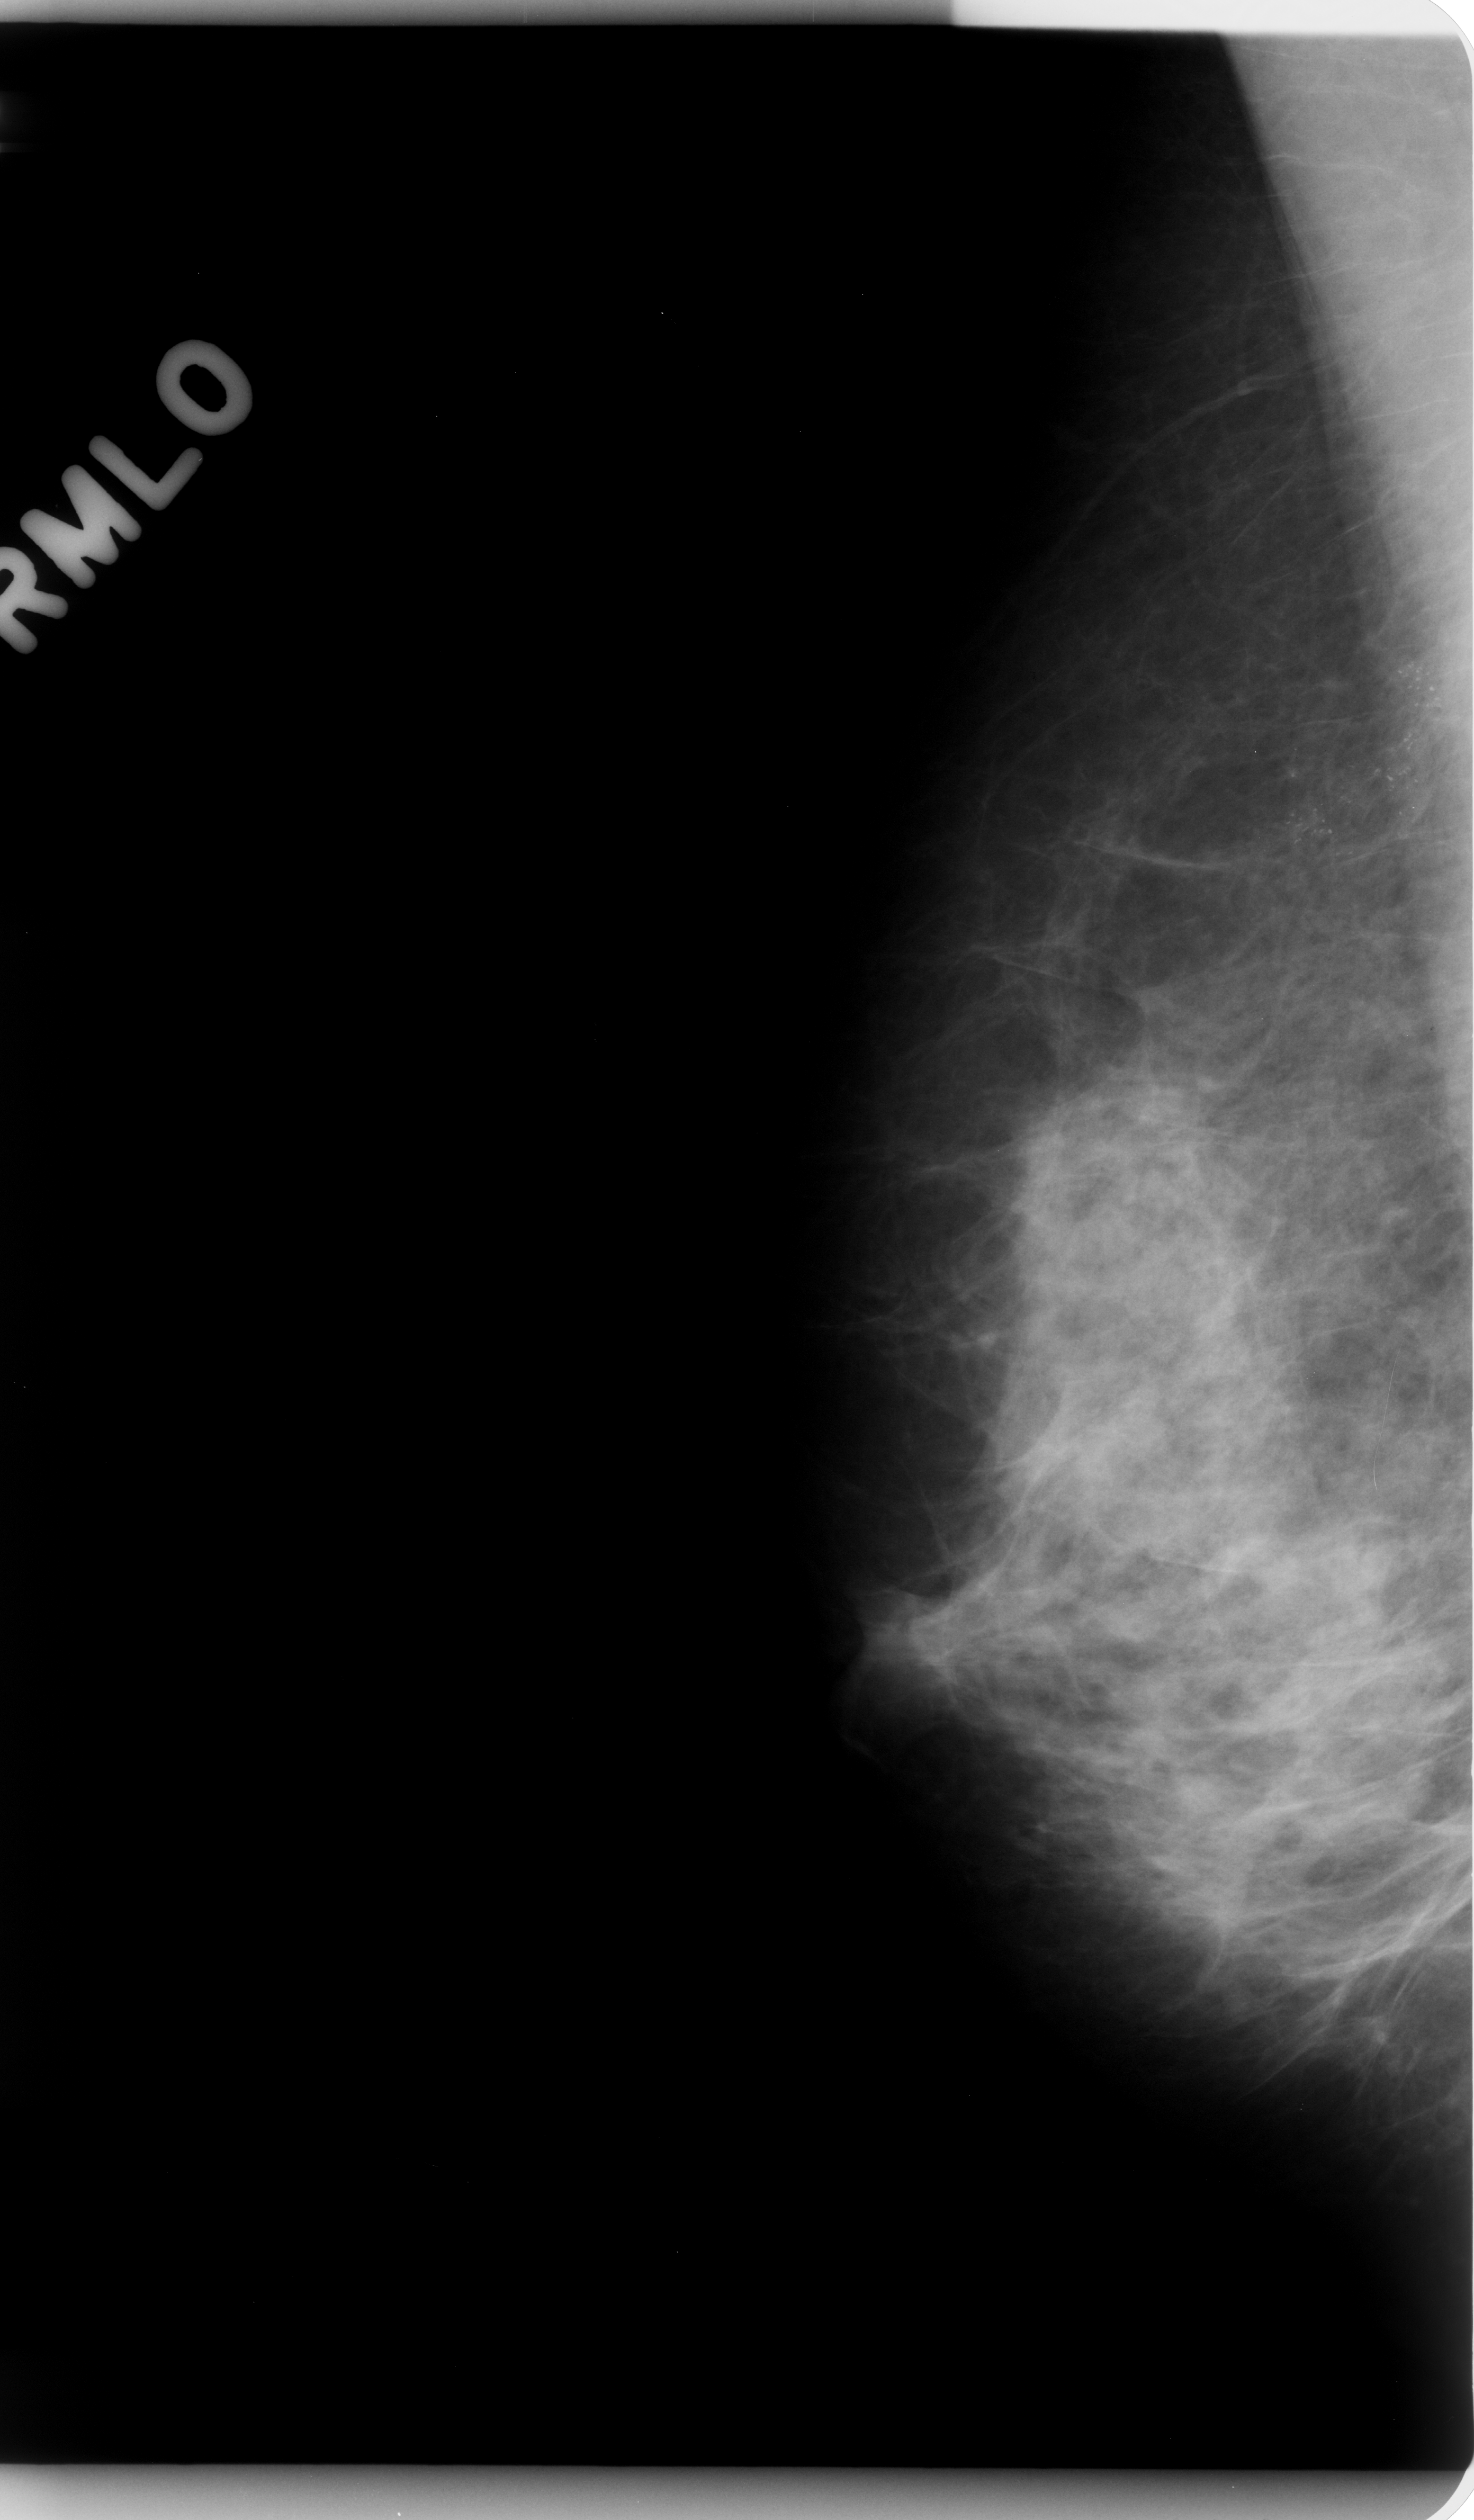
Scanned film-screen mammogram, right breast, mediolateral oblique (MLO) view, BI-RADS breast density category 3 (scale 1–4).
Finding: calcifications, morphology pleomorphic, distribution segmental; BI-RADS assessment category 5; pathology result (as recorded, not read from the image): malignant.